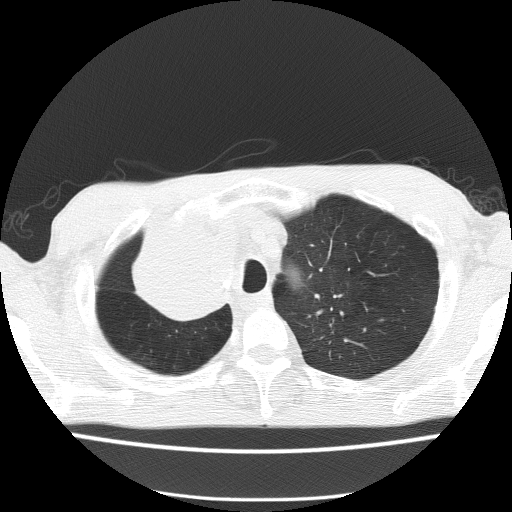
Chest CT (low-dose screening protocol), one axial image. First (baseline) screen. Lung window (W 1500 / L -600 HU). 512 × 512 image matrix, field of view 336 × 336 mm. Male participant, aged 59 years at enrolment. Former smoker at enrolment.
Expert reader's lesion annotation, bounding box [x1, y1, x2, y2] px = [128, 236, 241, 328]. The screening reader recorded 5 non-calcified nodules or masses ≥4 mm on this exam (left upper lobe, left upper lobe, left upper lobe, right middle lobe, right lower lobe); which of them this box marks is not recorded. Official screen result: positive, change unspecified: nodule(s) >= 4 mm or enlarging nodule(s), mass(es), or other non-specific abnormalities suspicious for lung cancer. Lung cancer was diagnosed 72 days after this screen: squamous cell carcinoma, NOS, right upper lobe, moderately differentiated (G2), stage IV (AJCC 6th edition).